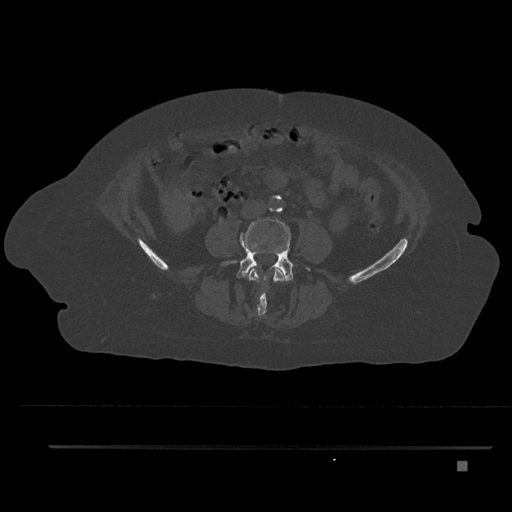
CT including the spine, one axial slice. Slice 94 of 797 in the series (ordered by position). Bone window (W 1800 / L 400 HU). 0.5 mm slice thickness. 512 × 512 image matrix, field of view 437 × 437 mm. Female patient, age 76 years. Case-level facts recorded for this patient, not image findings: primary cancer: lung.
Annotated regions visible in this slice (semi-automatically segmented with operator editing):
- L3 vertebra: bounding box (x1, y1, x2, y2) in pixels: (248, 267, 285, 316)
- L4 vertebra: (221, 217, 310, 289)